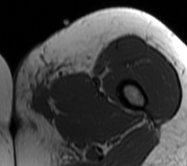
MRI of an extremity soft-tissue mass, one axial slice. Slice 12 of 62 in the series (ordered by position). MR volume resampled by the dataset authors to the PET/CT grid (not the native acquisition matrix). 3.27 mm slice thickness. 187 × 166 image matrix. Female patient. Case-level facts recorded for this patient, not image findings: histological type: leiomyosarcoma; grade: high; site of the primary tumour: groin.
Annotated regions visible in this slice (expert contour drawn on MRI and transferred to this co-registered scan by the dataset authors):
- gross tumour volume including surrounding oedema: bounding box (x1, y1, x2, y2) in pixels: (13, 55, 95, 123)